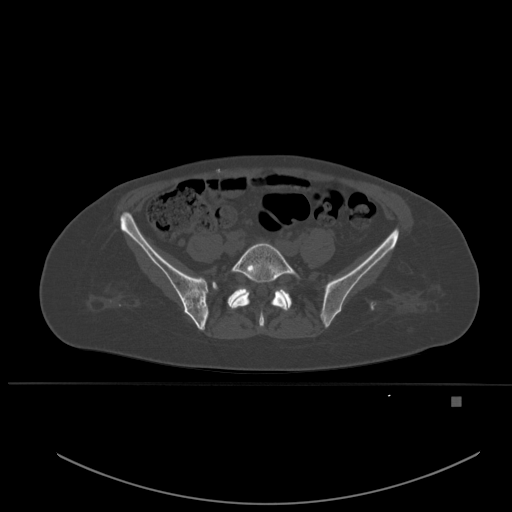
CT including the spine, one axial slice; position 150 of 651 along the scan axis; bone window (W 1800 / L 400 HU); 1.5 mm slice thickness; 512 × 512 image matrix, field of view 443 × 443 mm. Patient: female, 49 years. Case-level facts recorded for this patient, not image findings: primary cancer: breast.
Structures marked on this image (semi-automatic segmentation, software-assisted and operator-edited):
- L5 vertebra: bounding box <231,243,300,328> (left, top, right, bottom; pixels)